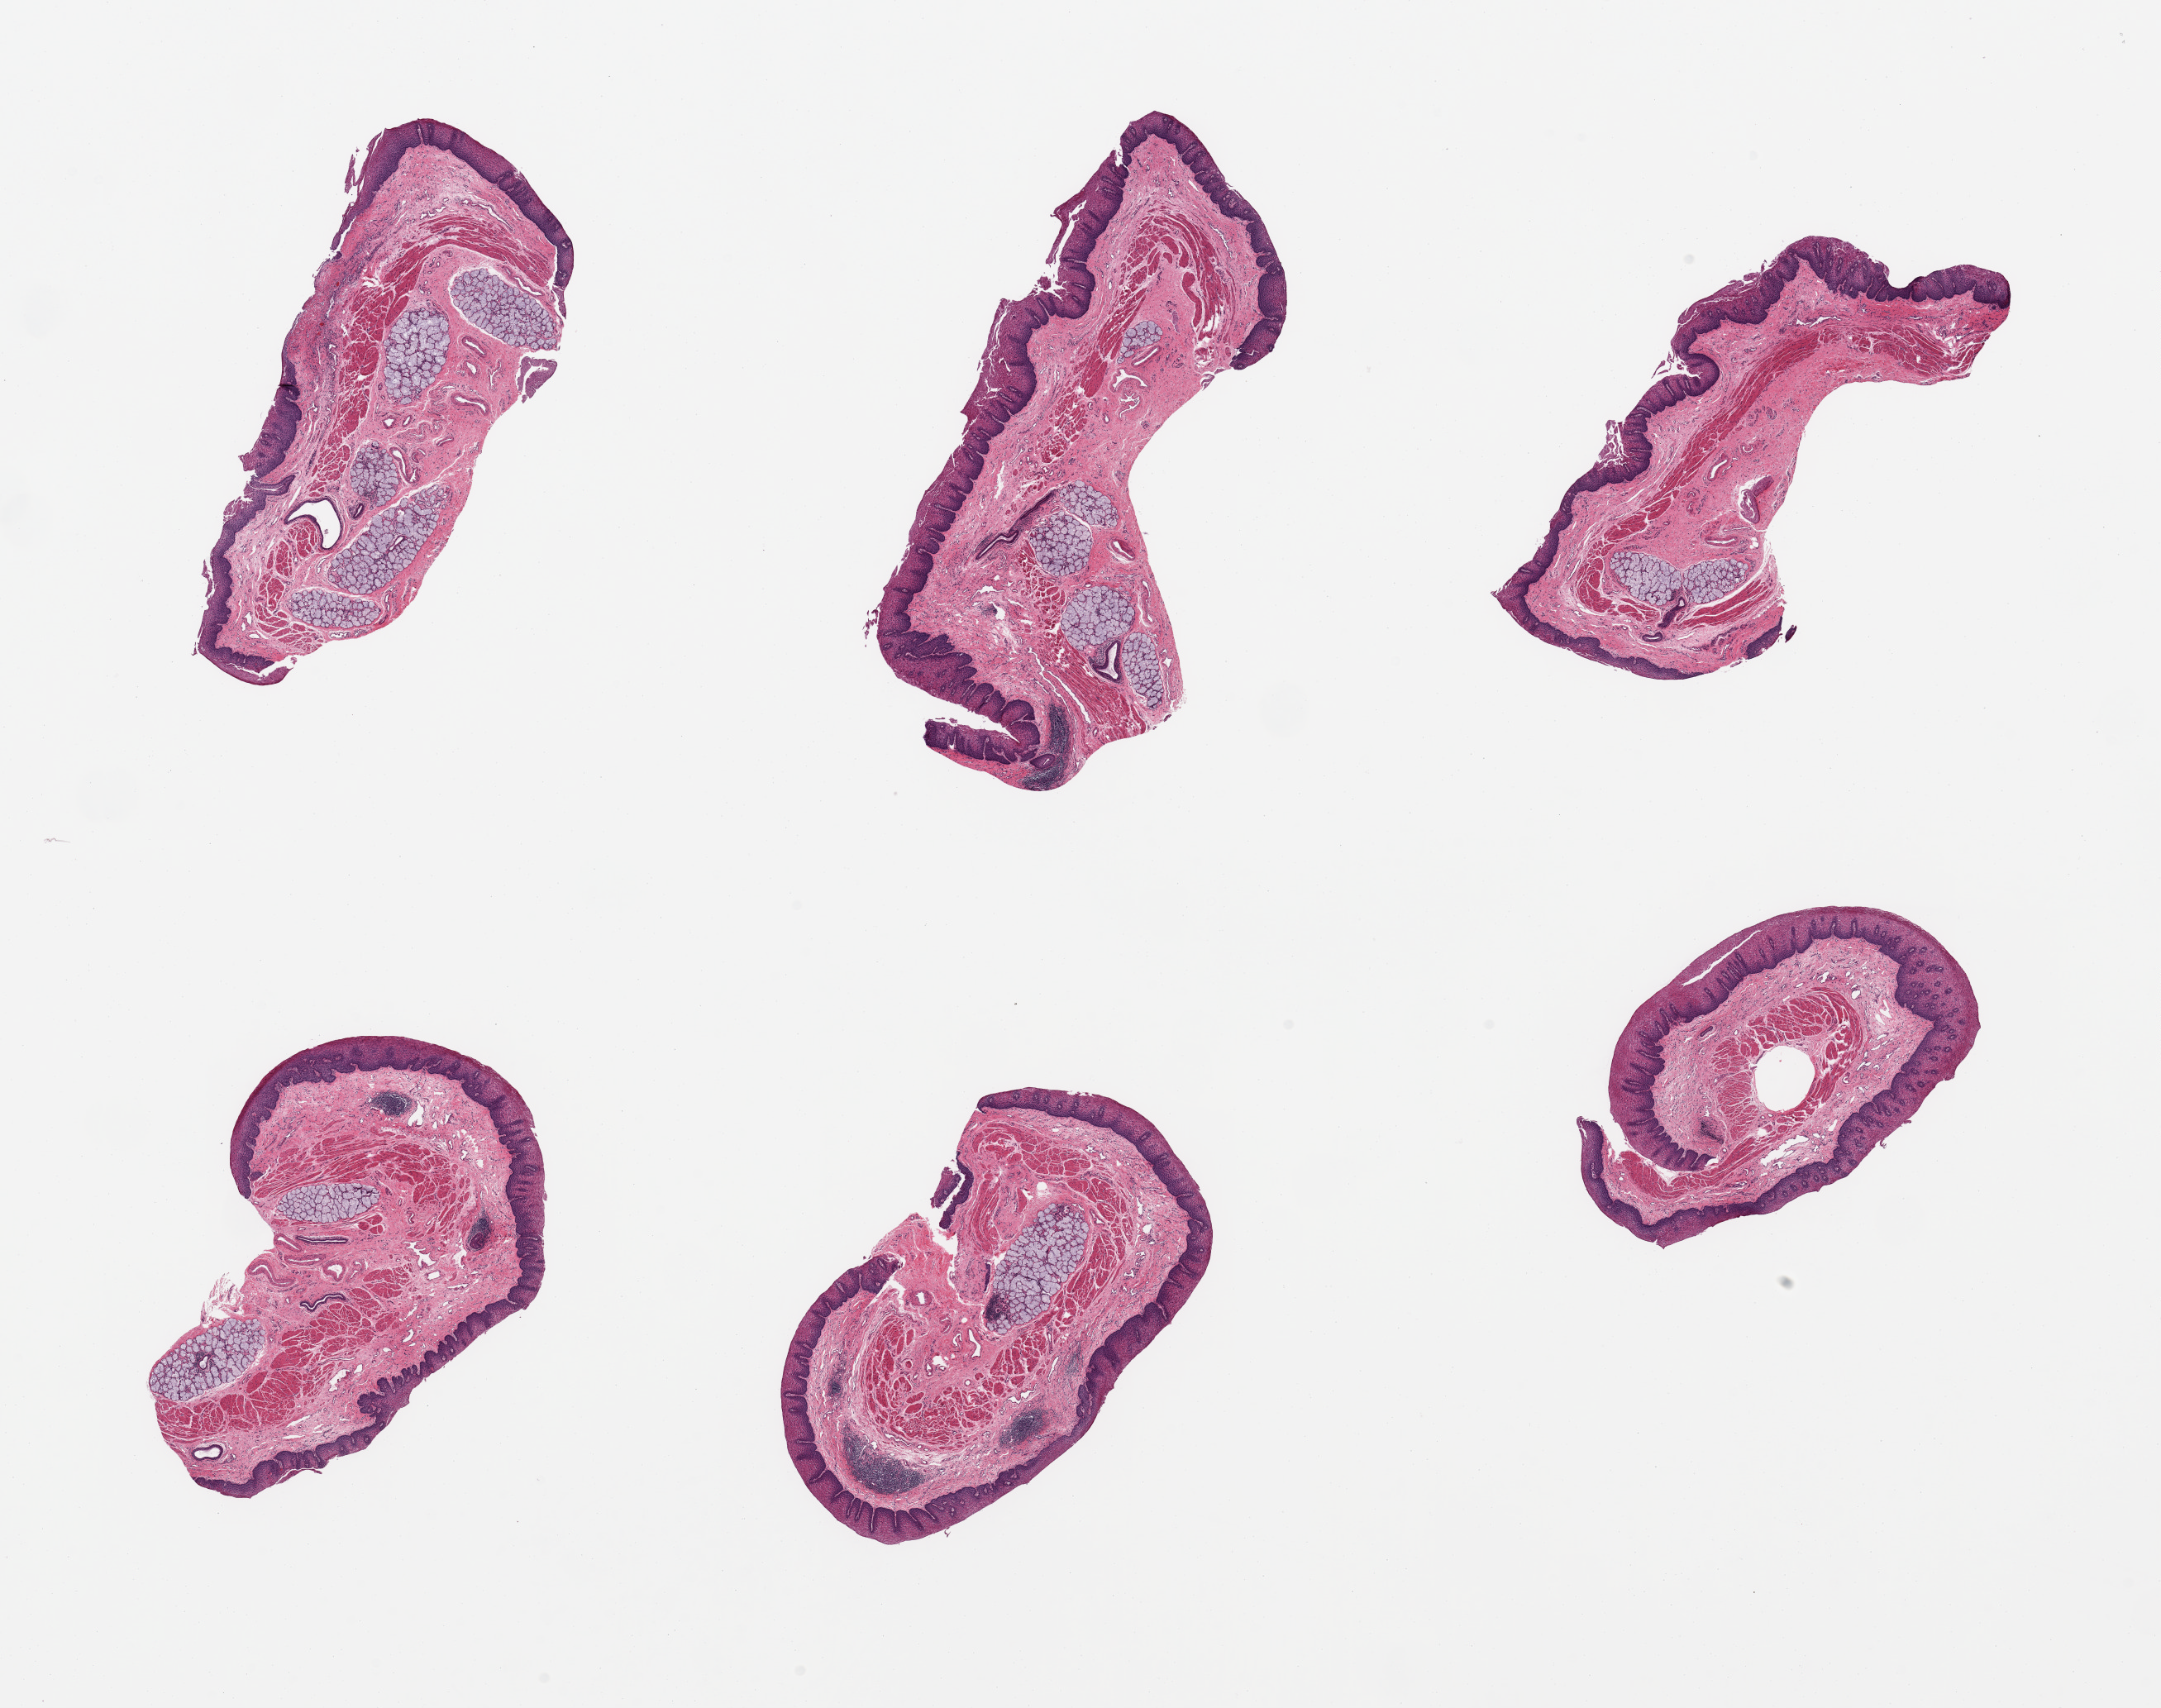
Digitized H&E-stained section — whole scanned area (about 20.7 x 16.3 mm, slide scanned at 20x) shown as a low-resolution overview, PAXgene-fixed, paraffin-embedded tissue, section of esophageal mucous membrane (target tissue), donor tissue sample. Donor sex: male.
* review note (as recorded): 6 pieces, squamous mucosa is ~0.3mm, ~10-20% thickness; prominent submucosal mucus glands